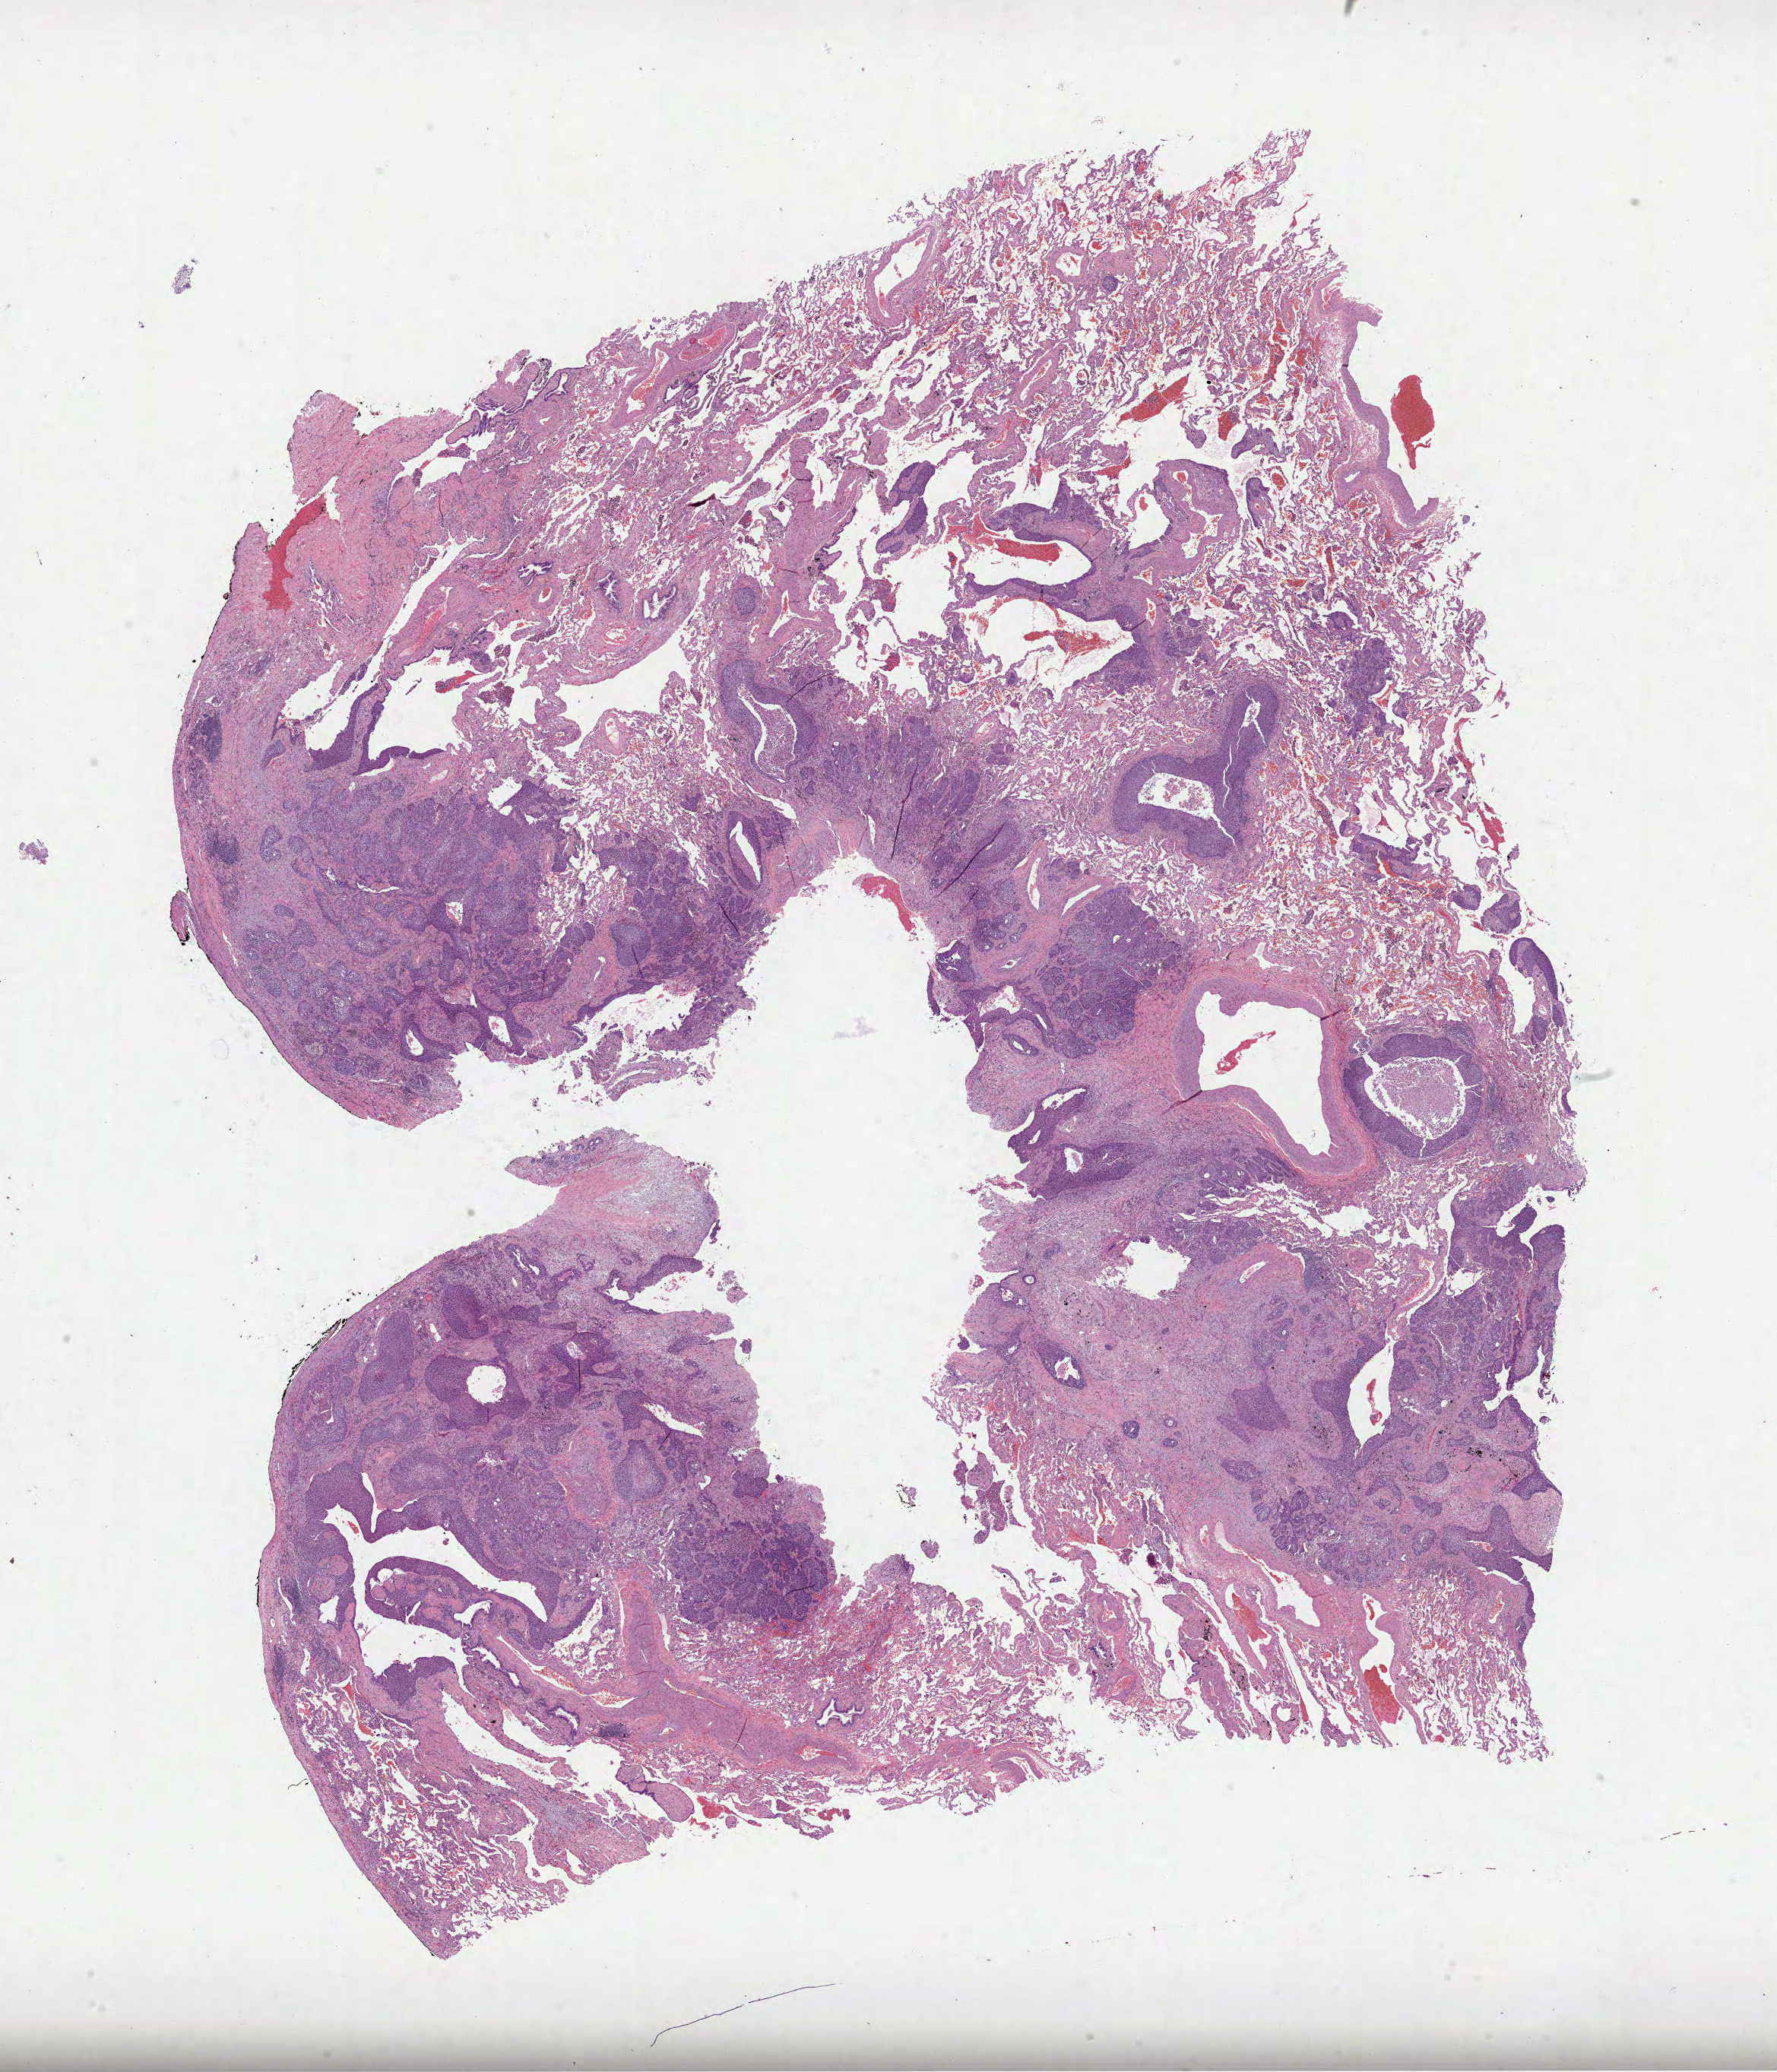
H&E whole-slide image — a low-resolution overview of the entire scanned area, about 18.9 x 22.0 mm (slide scanned at 40x), formalin-fixed paraffin-embedded (FFPE) diagnostic section, sample: primary tumour, lung. Male, age 71 years at initial diagnosis.
Diagnosis: Squamous cell carcinoma, NOS (upper lobe, lung).